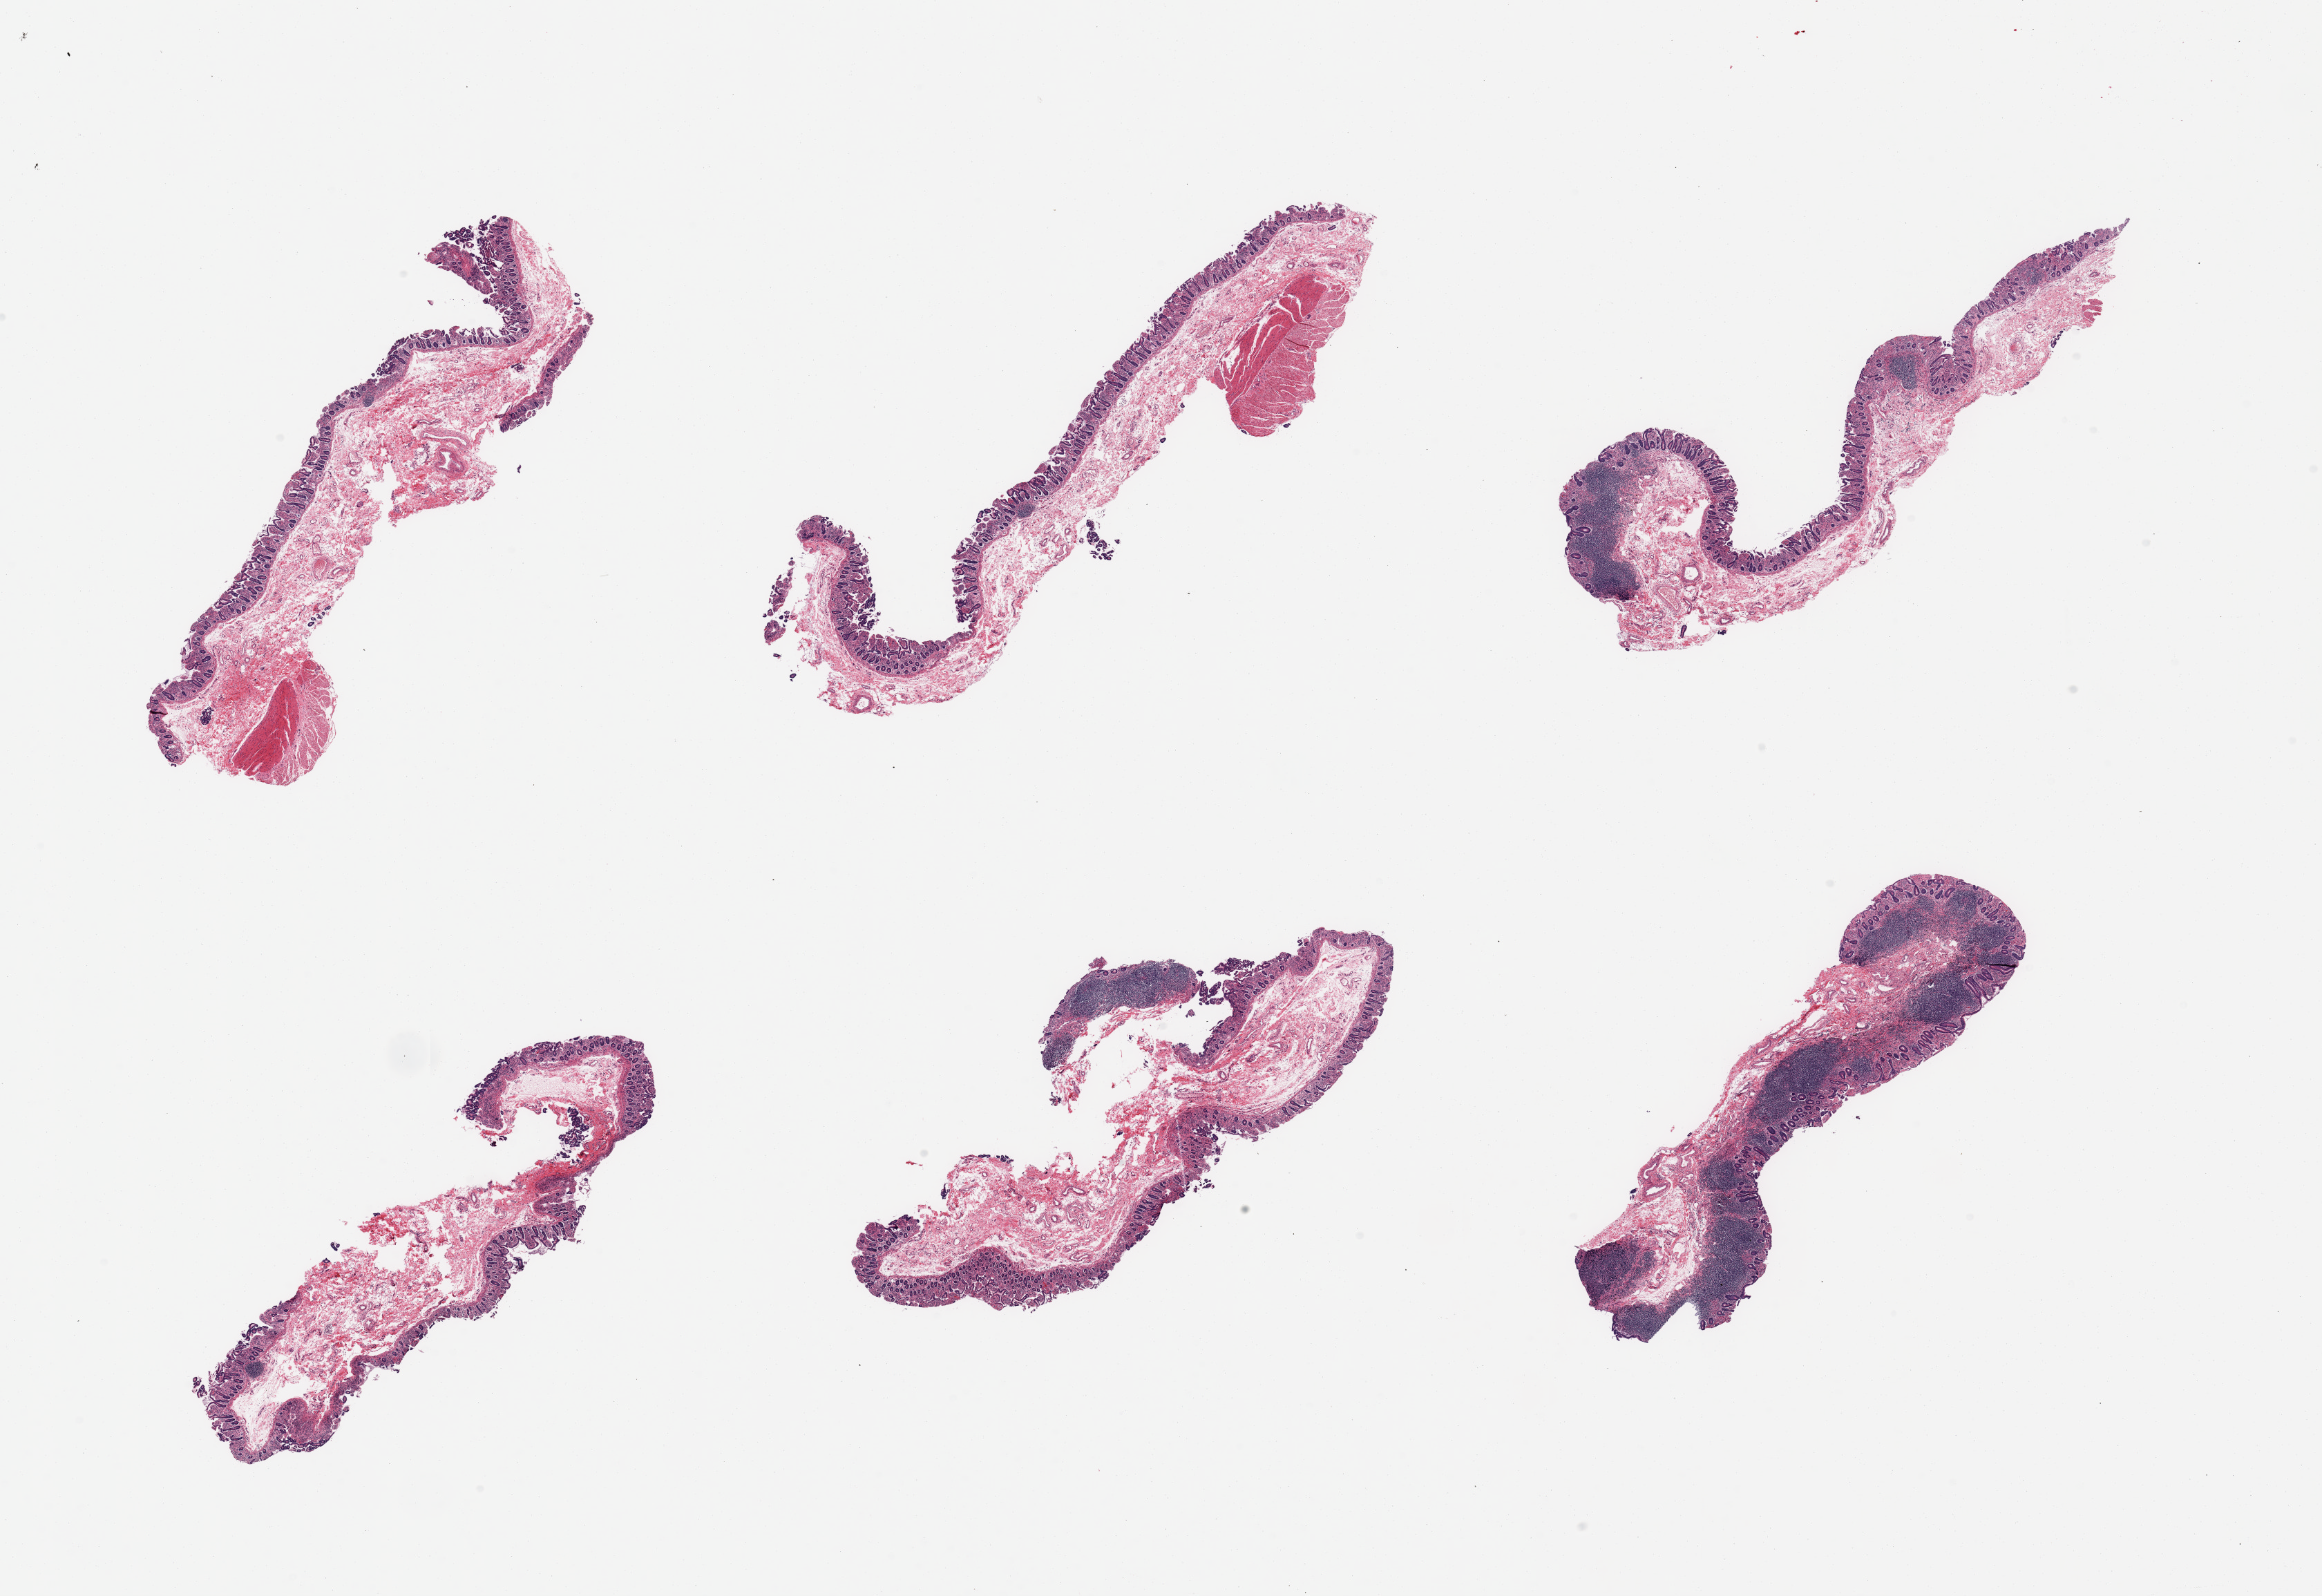
Whole-slide image, hematoxylin and eosin (H&E) stain, whole scanned area (about 26.6 x 18.3 mm) shown as a low-resolution overview. PAXgene-fixed, paraffin-embedded tissue. Target tissue: ileum. Donor tissue sample. Donor sex: female.
* reviewer comment on this tissue sample: 6 pieces; irregularly distributed target lymphoid aggregates in half of the pieces; well dissectedmucosa & sumucosa